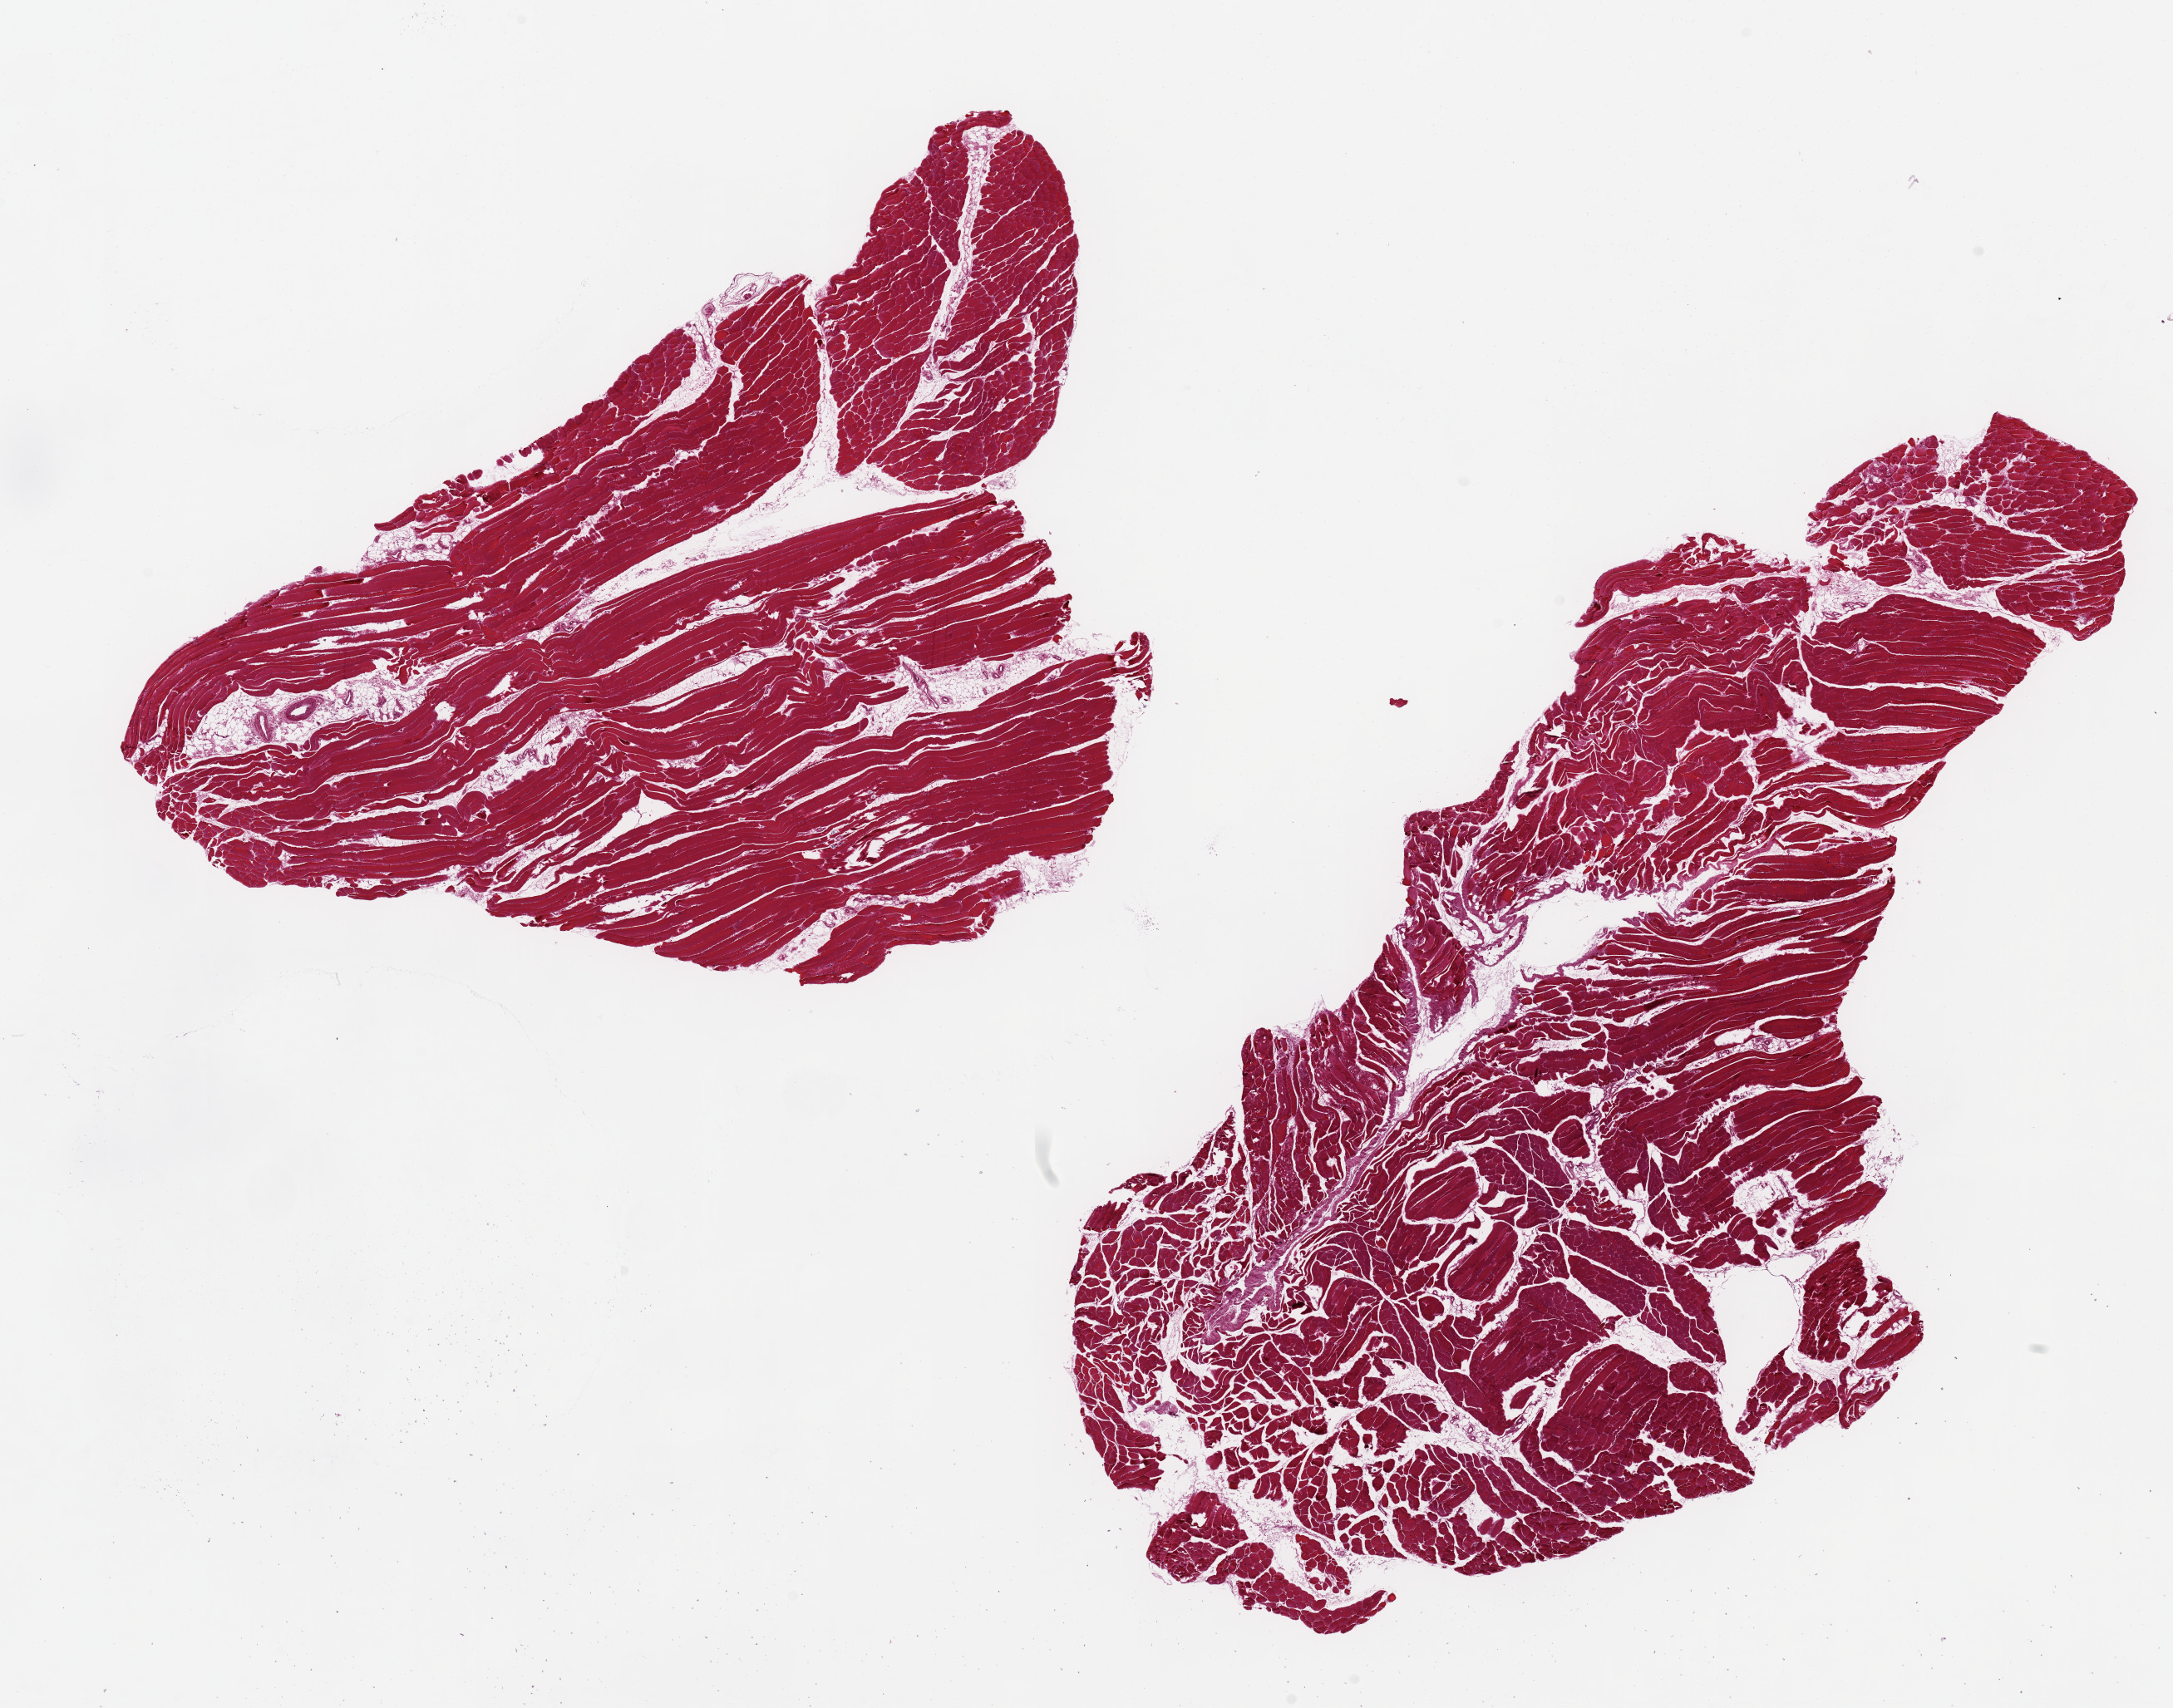
Whole-slide image, haematoxylin and eosin stain, brightfield, low-resolution overview of the scanned area, about 20.7 x 16.3 mm, PAXgene-fixed paraffin-embedded (PFPE) section, target tissue: skeletal muscle, donor tissue sample. Female donor.
Review note (as recorded): 2 pieces 13x6 & 10x6 mm; minimal adipose.